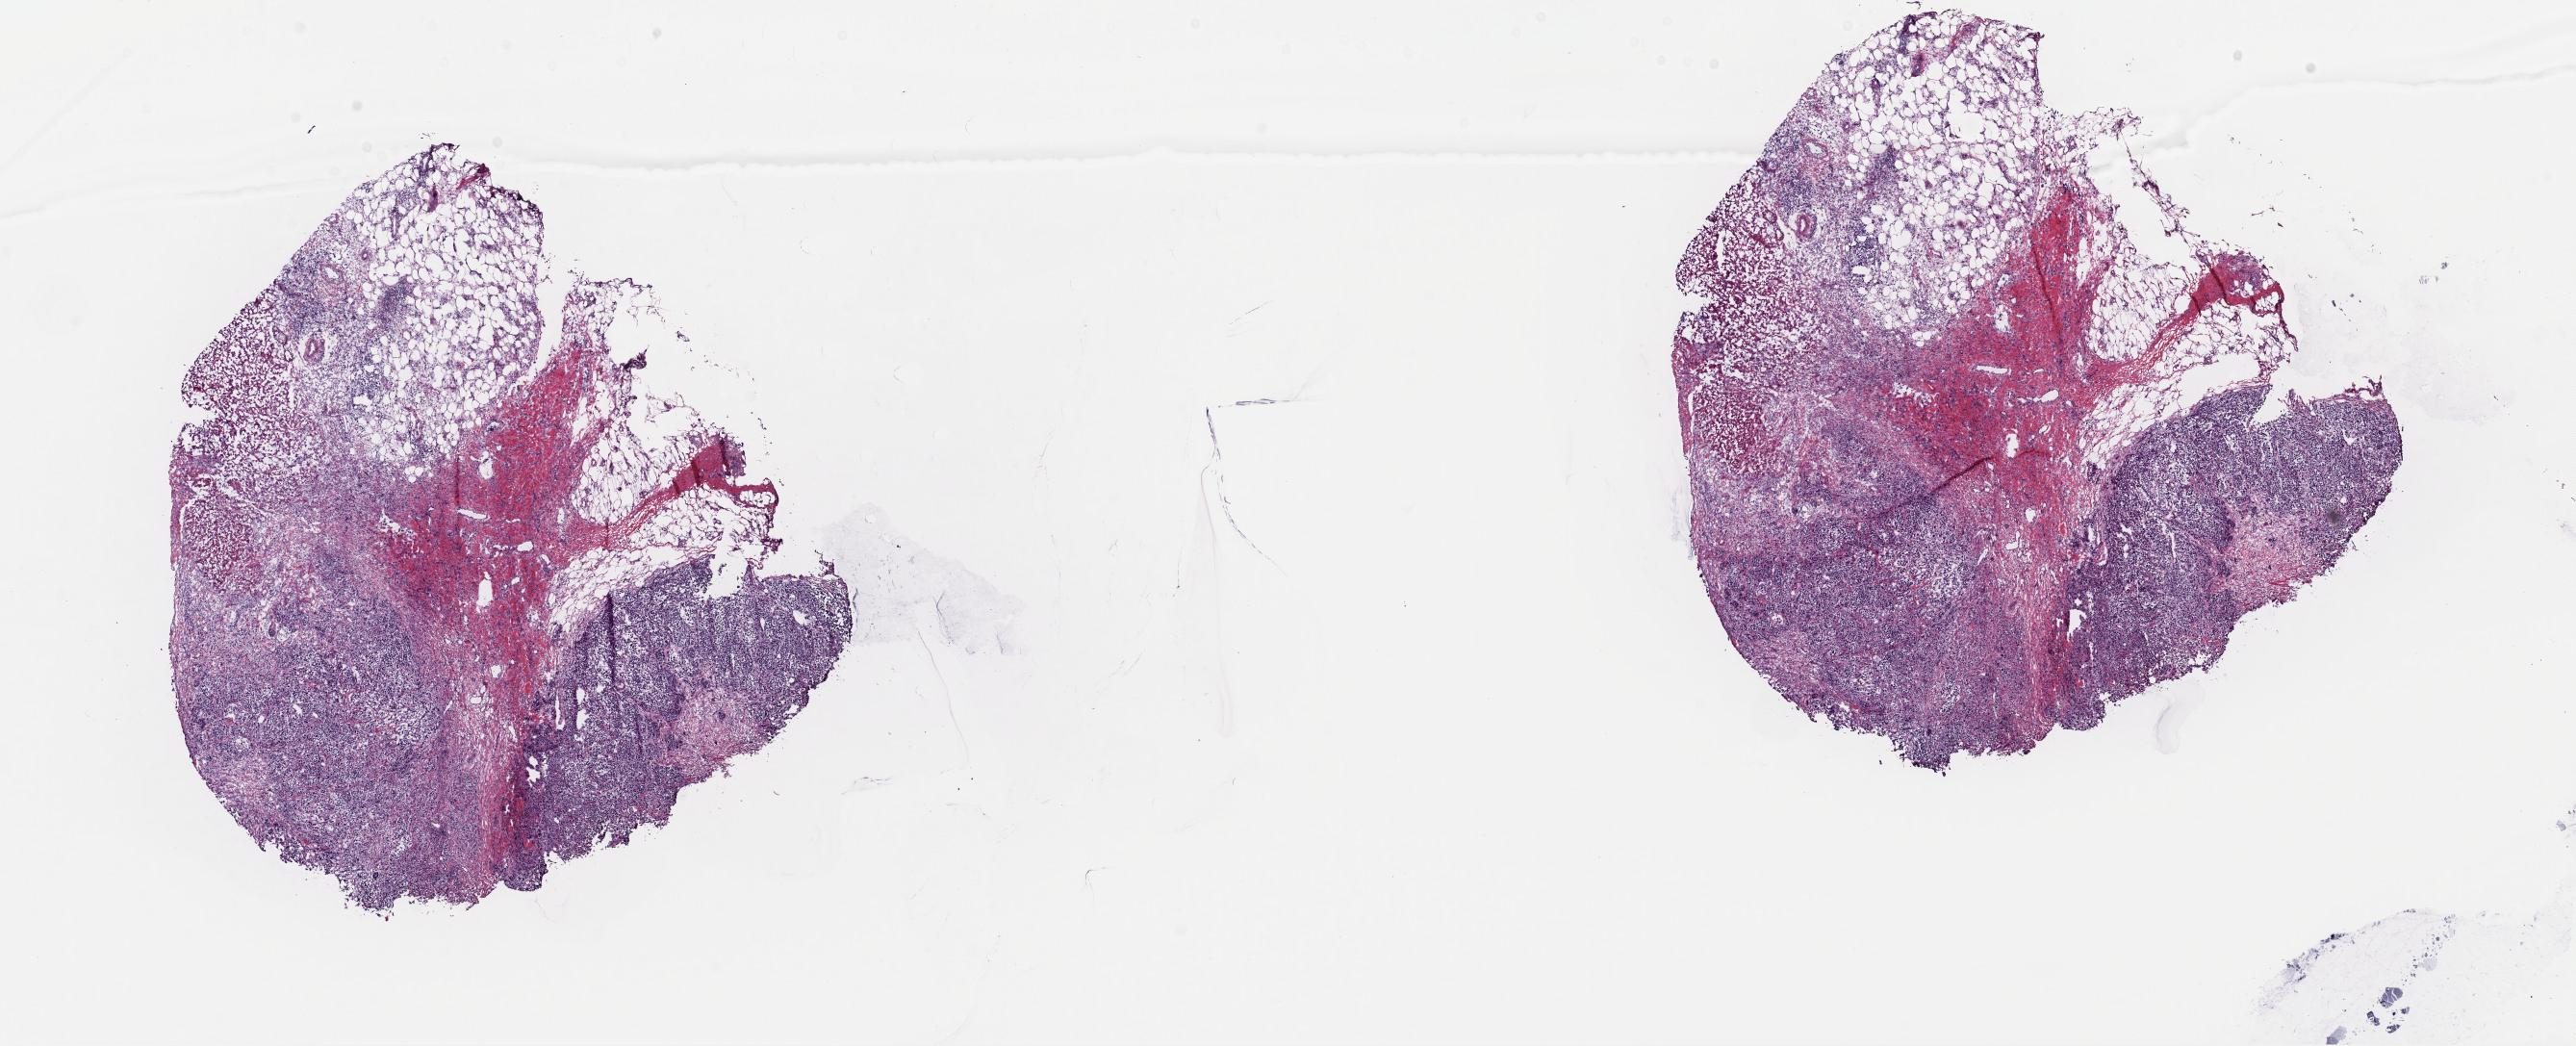
Digitized H&E tissue section (whole slide) — shown as a low-resolution overview of the whole scanned area (about 21.1 x 8.6 mm), frozen section from the top of the tissue portion, metastatic tumour sample, sampled site: connective, subcutaneous and other soft tissues. Female, age 39 years at initial diagnosis. Slide review estimates, as recorded: tumour cells 55%, tumour nuclei 65%, normal cells 10%, stromal cells 20%, necrosis 15%. Inflammatory infiltration, as recorded: lymphocyte infiltration 0%, monocyte infiltration 0%, neutrophil infiltration 0%.
This section: metastatic tumour tissue. Patient diagnosis: Malignant melanoma, NOS.